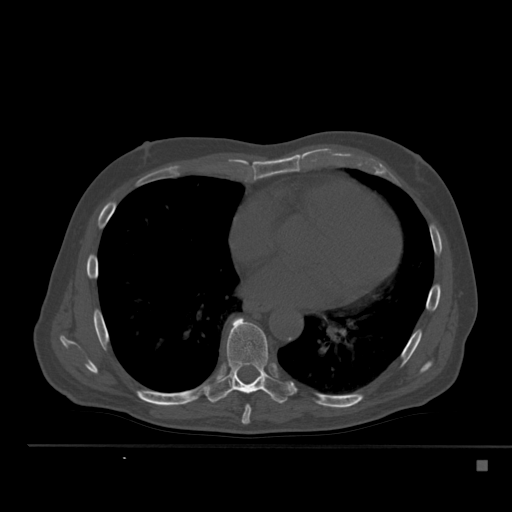
CT including the spine, one axial slice. Position 311 of 517 along the scan axis. 120 kVp. Bone window (W 1800 / L 400 HU). 512 × 512 image matrix, field of view 408 × 408 mm. Patient: male, 70 years. Case-level facts recorded for this patient, not image findings: primary cancer: renal; vertebrae with lytic lesions (as recorded): T4, T6, T10, T12, L3, L4, L5.
Annotated regions visible in this slice (semi-automatic segmentation, software-assisted and operator-edited):
- T7 vertebra: bounding box (x1, y1, x2, y2) in pixels: (241, 405, 251, 425)
- T8 vertebra: (204, 317, 290, 403)